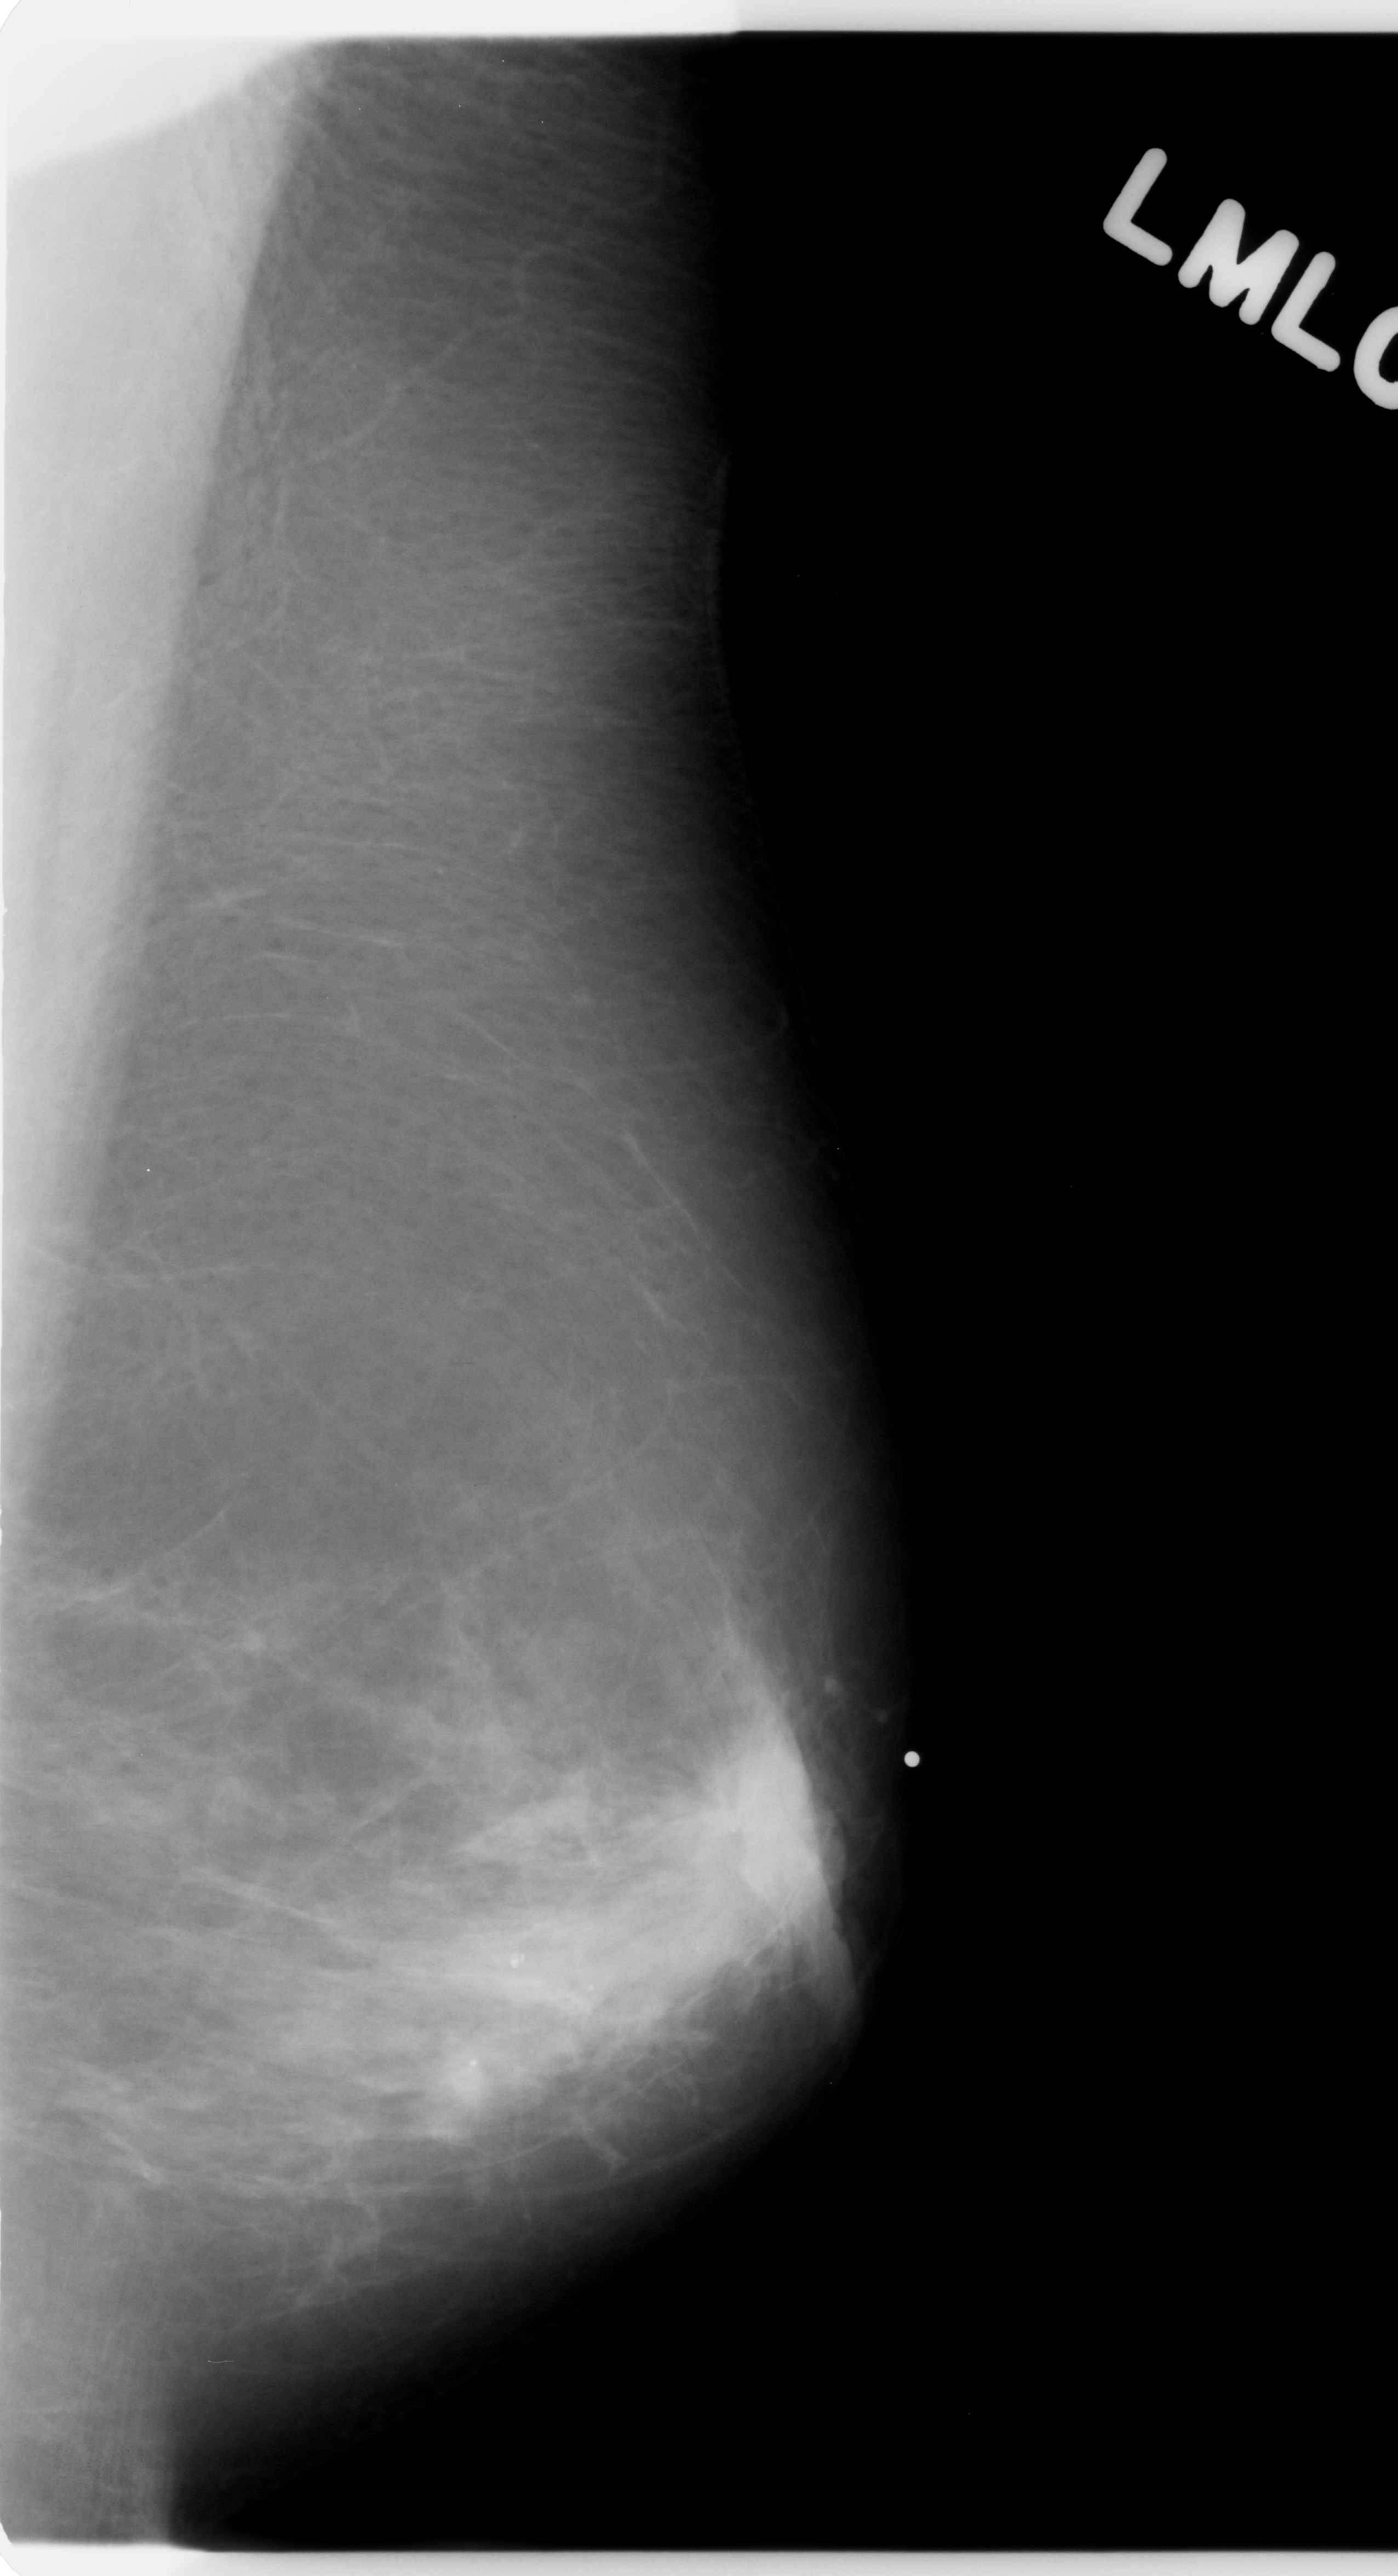
Scanned film-screen mammogram; left breast; mediolateral oblique (MLO) view; breast composition: scattered fibroglandular densities (BI-RADS density category 2 of 4).
Finding: mass, shape irregular, margins spiculated; BI-RADS assessment category 5; subtlety rating 5 on a 1 (subtle) to 5 (obvious) scale; pathology (as recorded): malignant.